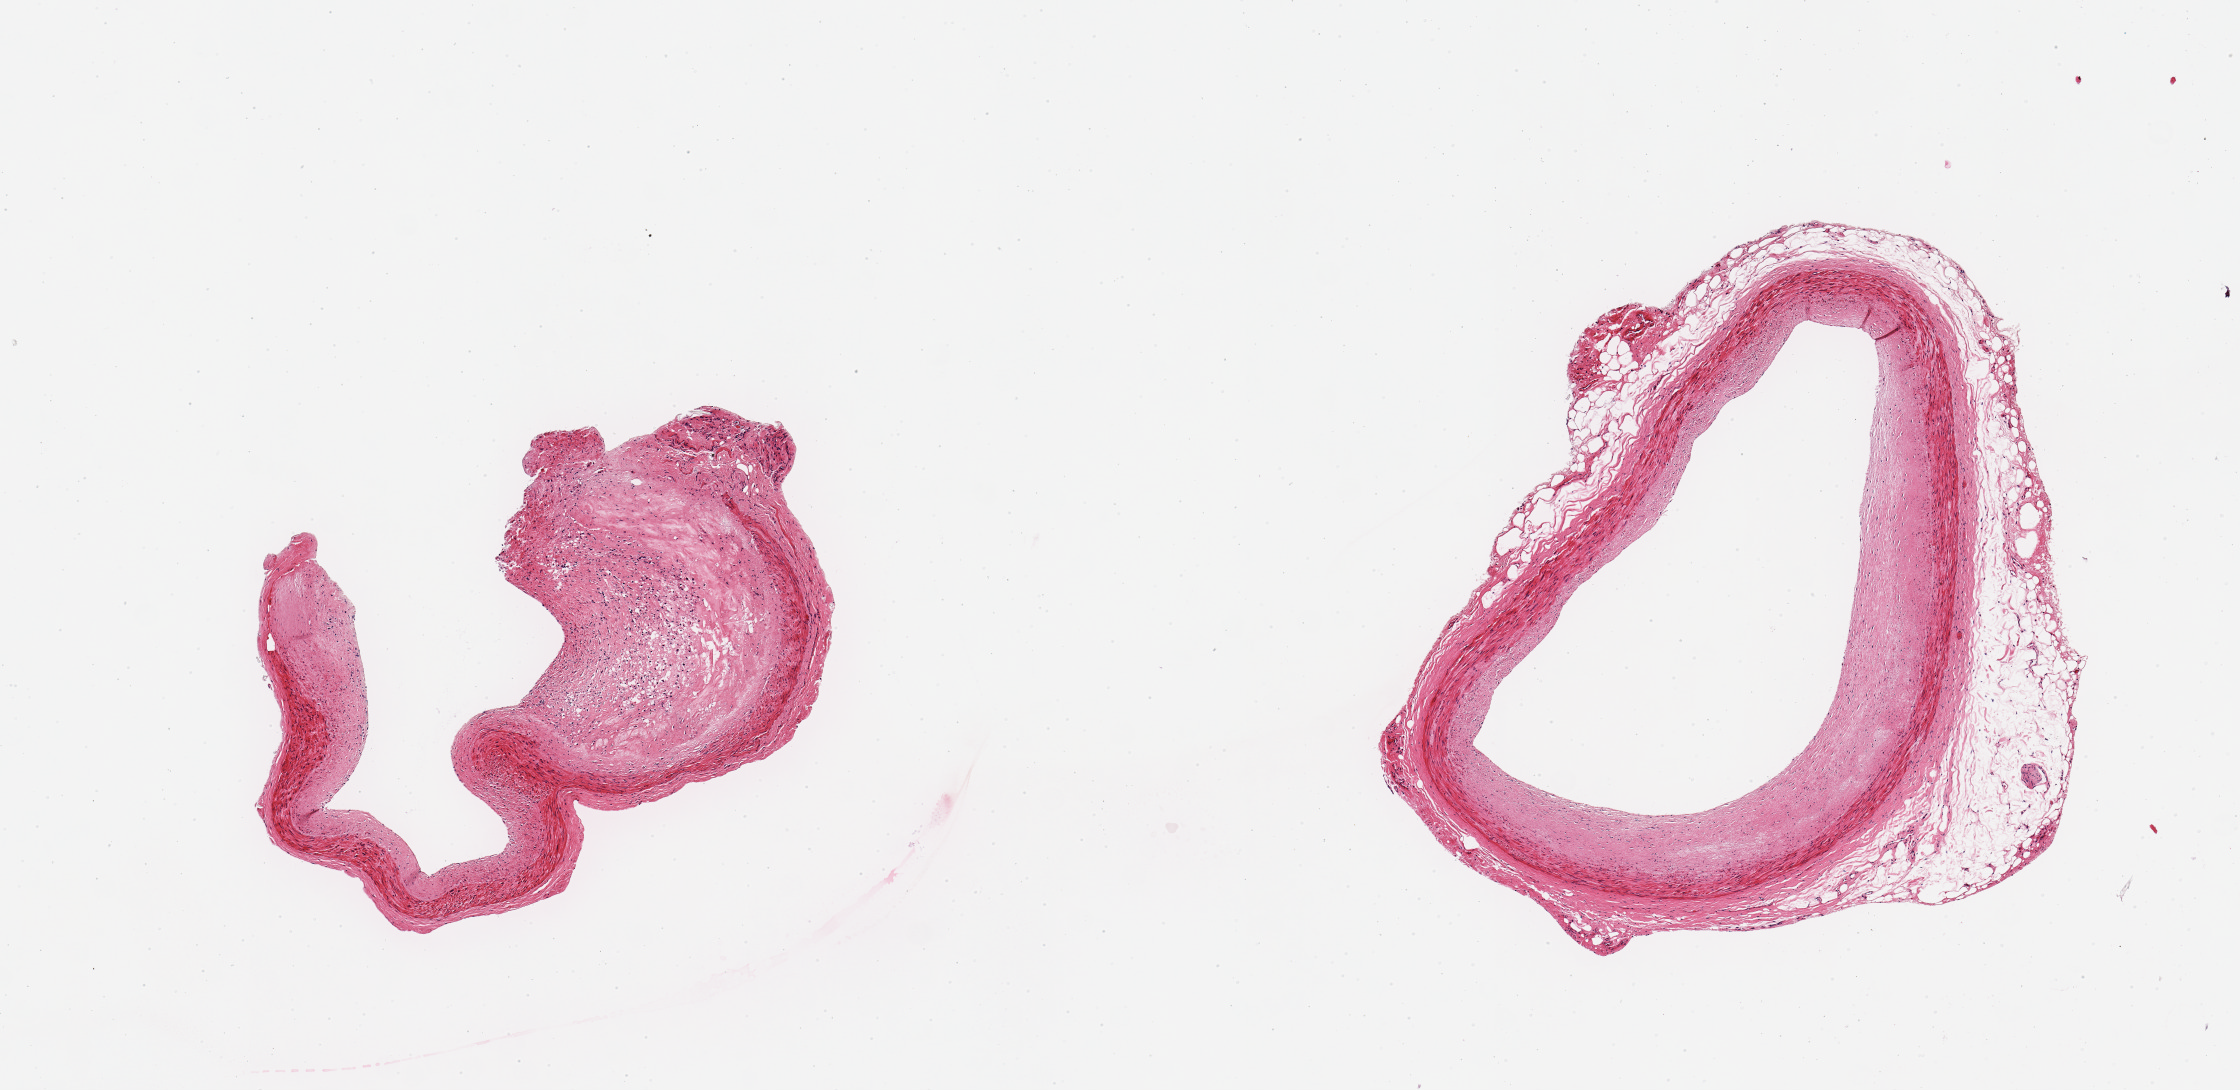
Hematoxylin and eosin (H&E) whole-slide image, a low-resolution overview of the entire scanned area, about 8.9 x 4.3 mm. PAXgene-fixed, paraffin-embedded tissue. Target tissue: coronary artery. Tissue donor sample. Male donor.
Review note (as recorded): 2 pieces, ~50% occlusive atherosis; adherent fat up to ~0.5mm.